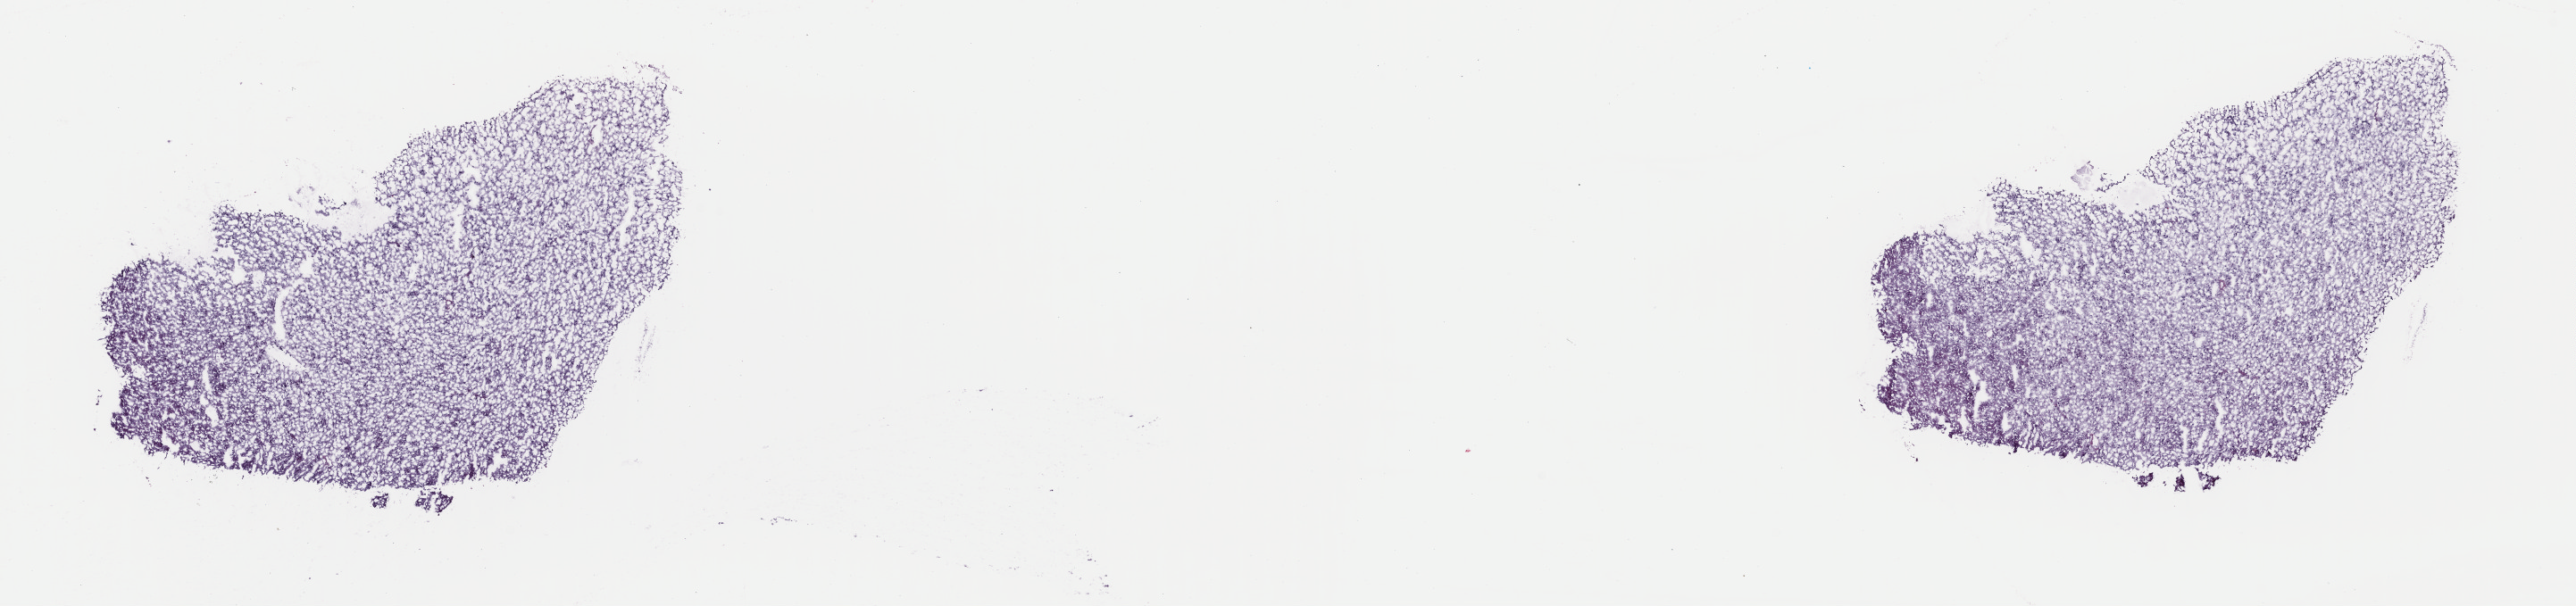
Whole-slide histology image, H&E, whole scanned area (about 22.8 x 5.4 mm) shown as a low-resolution overview, frozen section from the top of the tissue portion, brain, primary tumour sample. Male, age 24 years at initial diagnosis. Histologic grade: G2 (moderately differentiated). Composition of this section per pathologist review: tumour cells 50%, tumour nuclei 80%, normal cells 5%, stromal cells 45%, necrosis 0%. Inflammatory infiltration, as recorded: lymphocyte infiltration 0%, monocyte infiltration 0%, neutrophil infiltration 0%.
Pathologic diagnosis: Astrocytoma, NOS (cerebrum). Laterality: right.